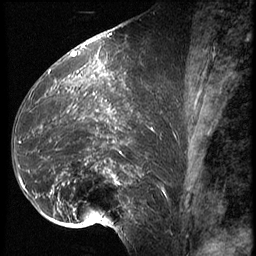
Breast MRI (dynamic contrast-enhanced), one sagittal slice. Slice 31 of 62 in the series (ordered by position). 3 images stored at this slice position (order not interpretable as contrast timing). 1.5 T. TE 4.2 ms, TR 9 ms. 2.5 mm slice thickness. 256 × 256 image matrix, field of view 180 × 180 mm. Female patient, age 39 years. Case-level facts recorded for this patient, not image findings: setting: breast cancer imaged before/during neoadjuvant chemotherapy; receptor status: HER2-positive.
Outlined on this slice (semi-automatic segmentation, software-assisted and operator-edited):
- analysis volume of interest (the breast-tissue region the enhancement analysis was run in; not a lesion): bounding box (x1, y1, x2, y2) in pixels: (16, 64, 169, 228)
- tumour enhancement mask (voxels above the 140 % enhancement threshold inside the analysis volume of interest): (19, 81, 156, 225)